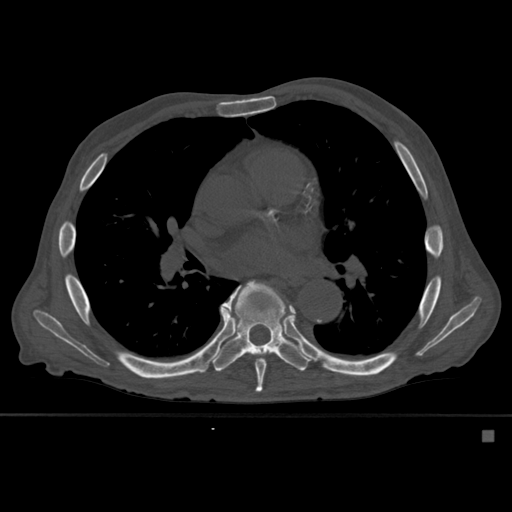
CT including the spine, one axial slice. Position 357 of 527 along the scan axis. Bone window (W 1800 / L 400 HU). 1.5 mm slice thickness. 512 × 512 image matrix, field of view 373 × 373 mm. Patient: male, 78 years. Case-level facts recorded for this patient, not image findings: primary cancer: prostate.
Annotated regions visible in this slice (semi-automatically segmented with operator editing):
- T7 vertebra: bounding box (x1, y1, x2, y2) in pixels: (224, 280, 296, 393)
- T8 vertebra: (211, 282, 310, 372)